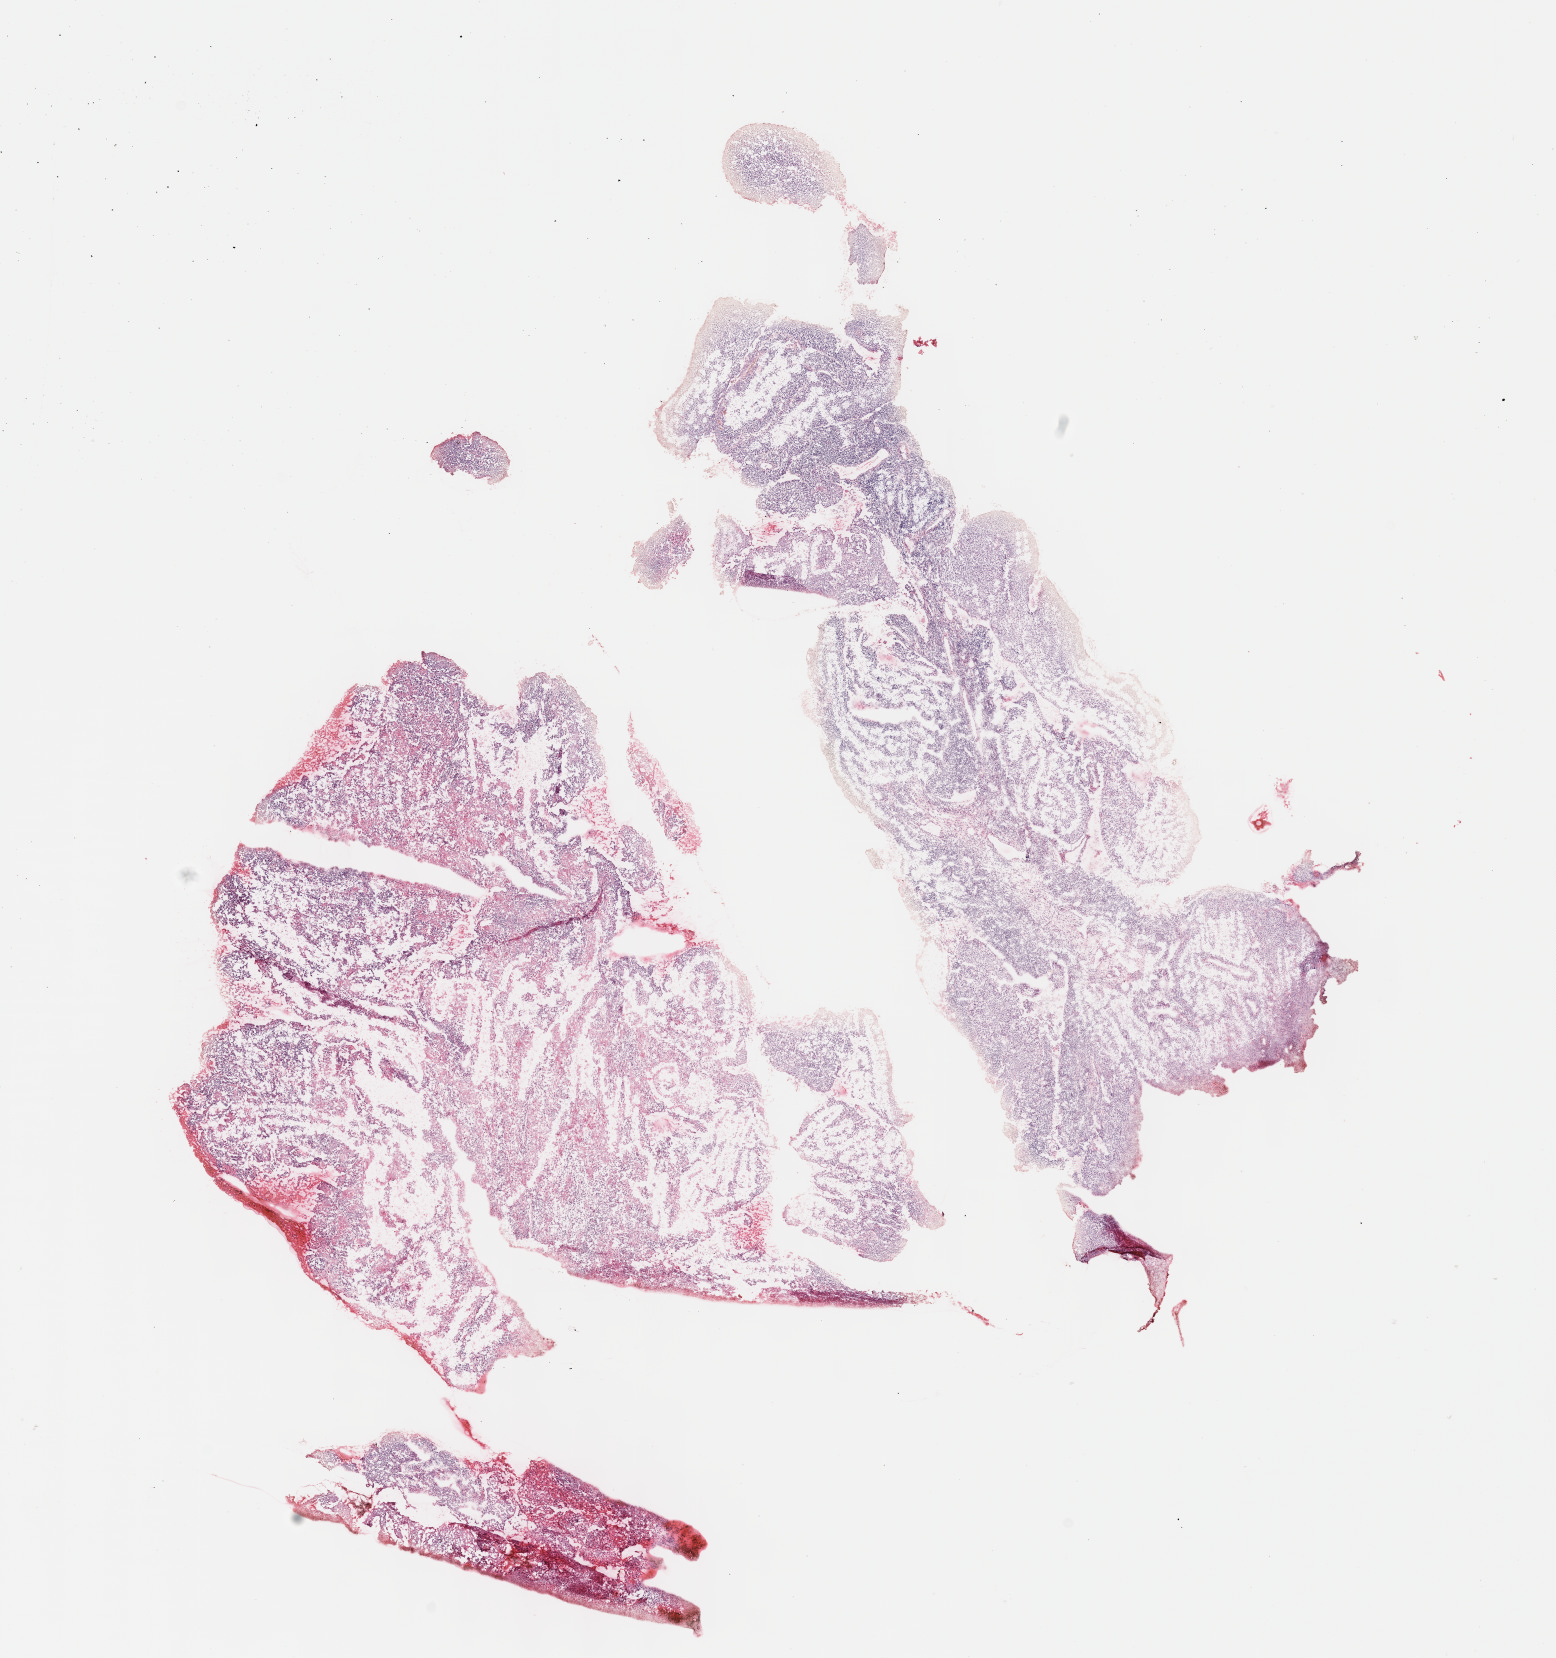
Digitized H&E-stained tissue section (whole slide) — low-resolution overview of the scanned area, about 12.6 x 13.4 mm (from a 40x scan), formalin-fixed paraffin-embedded (FFPE) diagnostic section, cervix, primary tumour sample. Patient: female, age at initial diagnosis 32 years. Histologic grade: G2 (moderately differentiated).
* diagnosis: Squamous cell carcinoma, NOS (cervix uteri)
* FIGO stage: IB